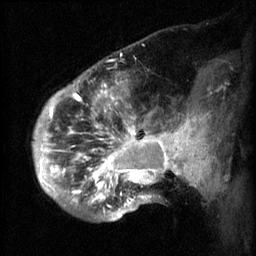
Breast MRI (dynamic contrast-enhanced), one sagittal slice. Slice 17 of 60 in the series (ordered by position). 3 images stored at this slice position (order not interpretable as contrast timing). 1.5 T. TE 4.2 ms, TR 8.2 ms. 2.3 mm slice thickness. 256 × 256 image matrix, field of view 200 × 200 mm. Patient: female, 50 years.
Structures marked on this image (semi-automatic segmentation, software-assisted and operator-edited):
- analysis volume of interest (the breast-tissue region the enhancement analysis was run in; not a lesion): bounding box <50,64,169,217> (left, top, right, bottom; pixels)
- tumour enhancement mask (voxels above the 70 % enhancement threshold inside the analysis volume of interest): <50,82,169,207>